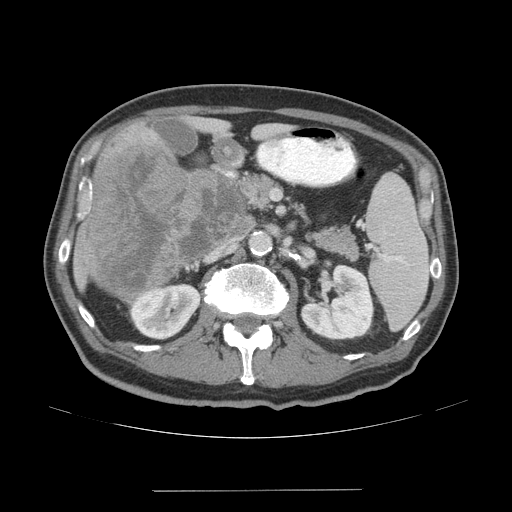
Contrast-enhanced abdominal CT (liver protocol), one axial slice; slice 19 of 77 in the series (ordered by position); 140 kVp; soft-tissue window (W 400 / L 40 HU); 2.5 mm slice thickness; 512 × 512 image matrix, field of view 400 × 400 mm. From the clinical record (not read from this slice): diagnosis: hepatocellular carcinoma (patient treated with transarterial chemoembolisation; whether this scan precedes or follows treatment is not stated here); TNM stage (as recorded): Stage-IVA; Child-Pugh class: A; tumour differentiation: well differentiated.
Annotated regions visible in this slice (semi-automatically segmented with operator editing):
- liver parenchyma outside the tumour (the mass and vessels are separate outlines, so this box may not span the whole liver): bounding box (x1, y1, x2, y2) in pixels: (74, 124, 246, 302)
- mass: (87, 142, 245, 299)
- liver vessels: (89, 183, 92, 197)